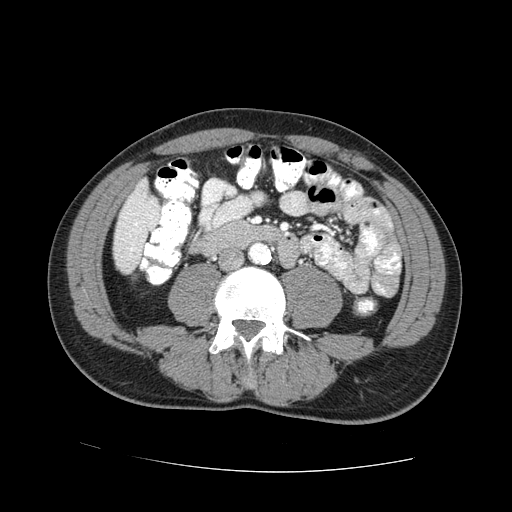
Contrast-enhanced abdominal CT (liver protocol), one axial slice; slice 7 of 73 in the series (ordered by position); one of 2 acquisitions stored at this slice position; soft-tissue window (W 400 / L 40 HU); 2.5 mm slice thickness; 512 × 512 image matrix, field of view 380 × 380 mm. From the clinical record (not read from this slice): diagnosis: hepatocellular carcinoma (patient treated with transarterial chemoembolisation; whether this scan precedes or follows treatment is not stated here); TNM stage (as recorded): Stage-IVA; Child-Pugh class: A; tumour nodularity: uninodular.
Annotated regions visible in this slice (semi-automatically segmented with operator editing):
- liver parenchyma outside the tumour (the mass and vessels are separate outlines, so this box may not span the whole liver): bounding box [x1, y1, x2, y2] px = [114, 178, 160, 272]
- liver vessels: [131, 223, 137, 250]